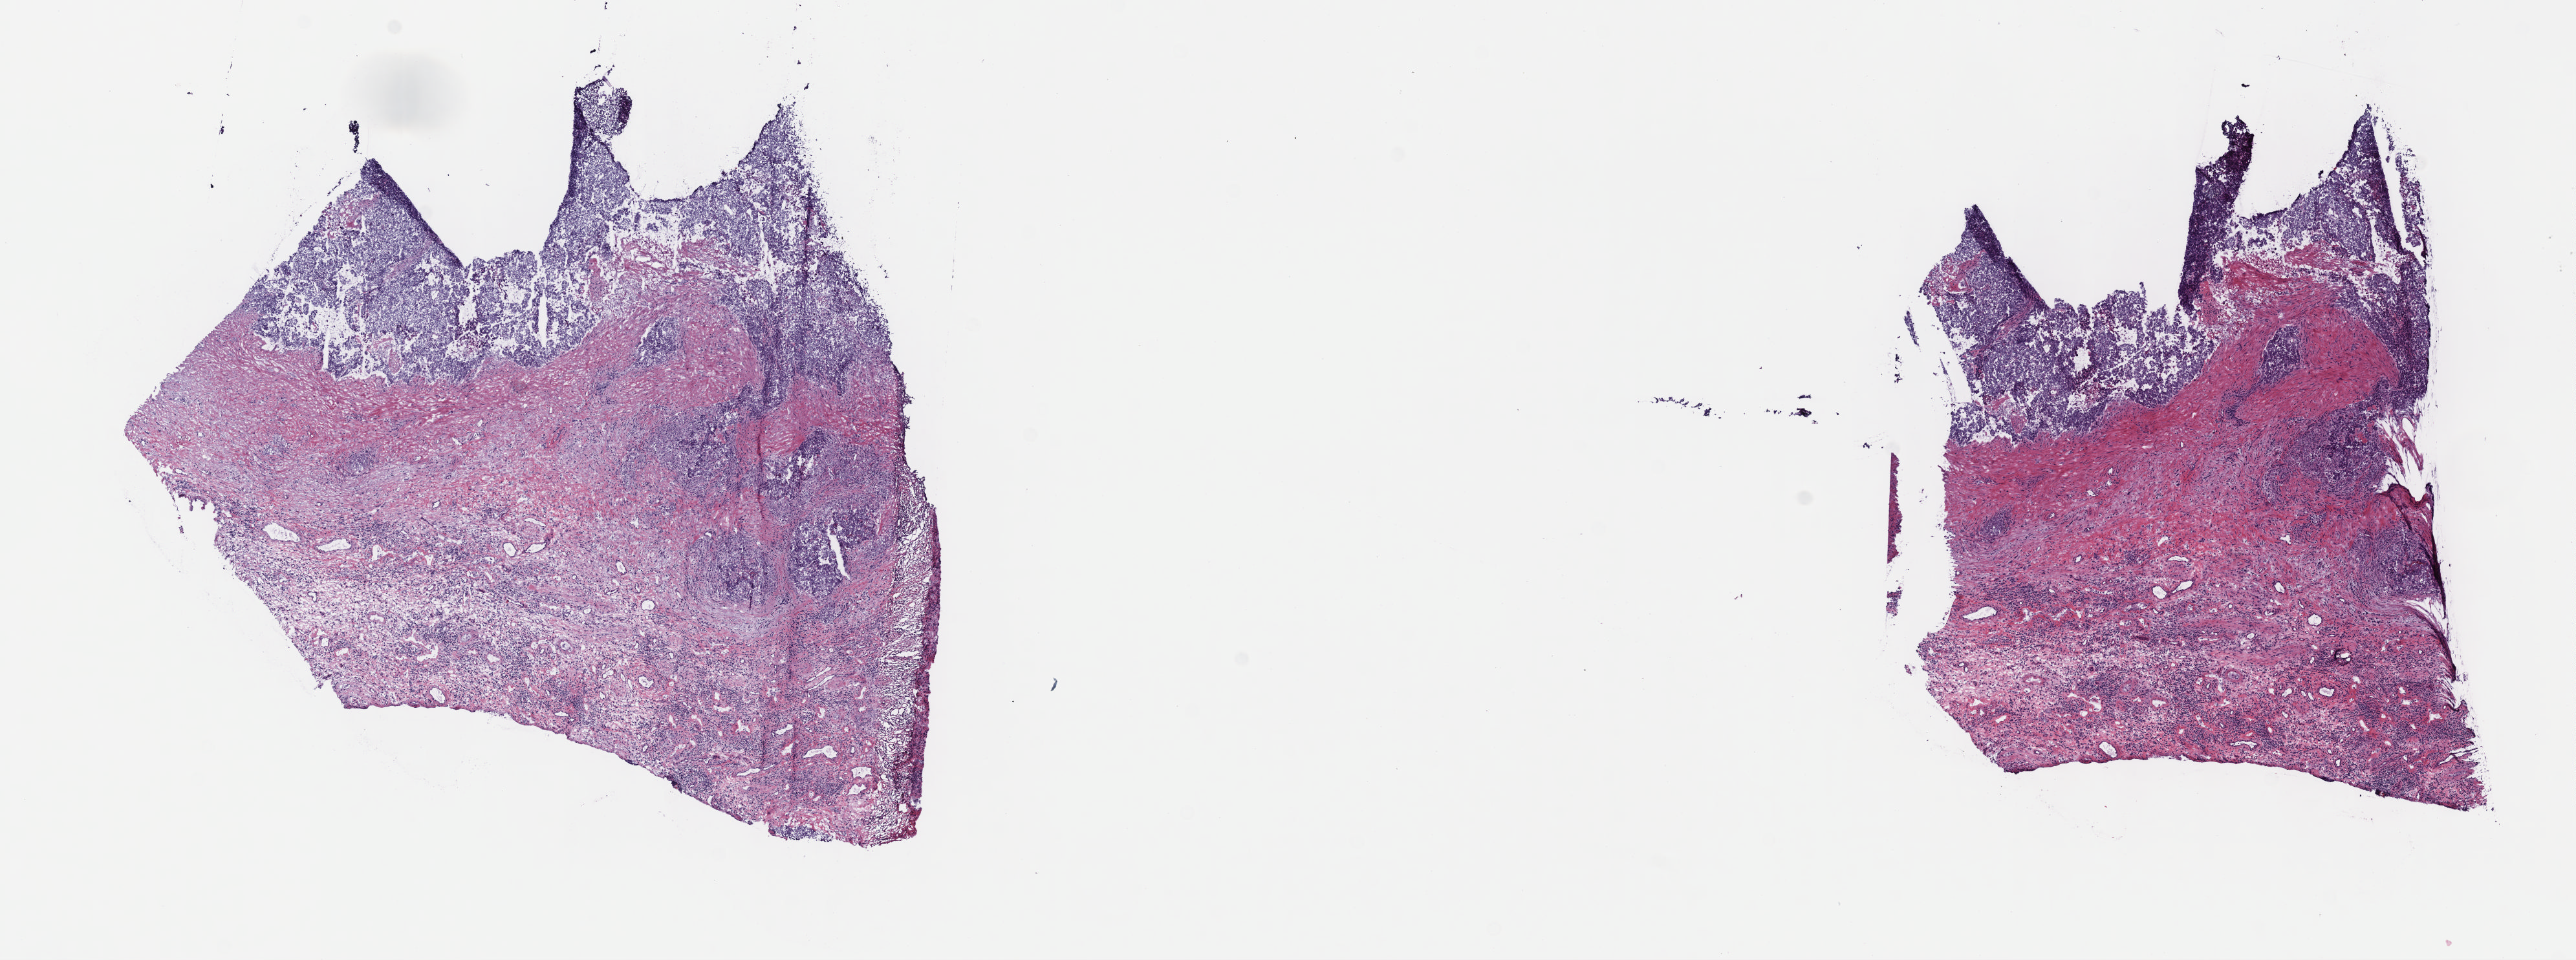
Whole-slide histology image, H&E — a low-resolution overview of the entire scanned area, about 16.1 x 6.0 mm (slide scanned at 40x); frozen section from the top of the tissue portion; sample: primary tumour, testis. Patient: male, age at initial diagnosis 27 years. Slide review estimates, as recorded: tumour cells 100%, tumour nuclei 60%, normal cells 0%, stromal cells 0%, necrosis 0%. Infiltration values recorded for this section: lymphocyte infiltration 4%, monocyte infiltration 0%, neutrophil infiltration 0%.
* laterality: left
* AJCC pathologic stage: IIIA (5th edition)
* pathologic diagnosis: Embryonal carcinoma, NOS